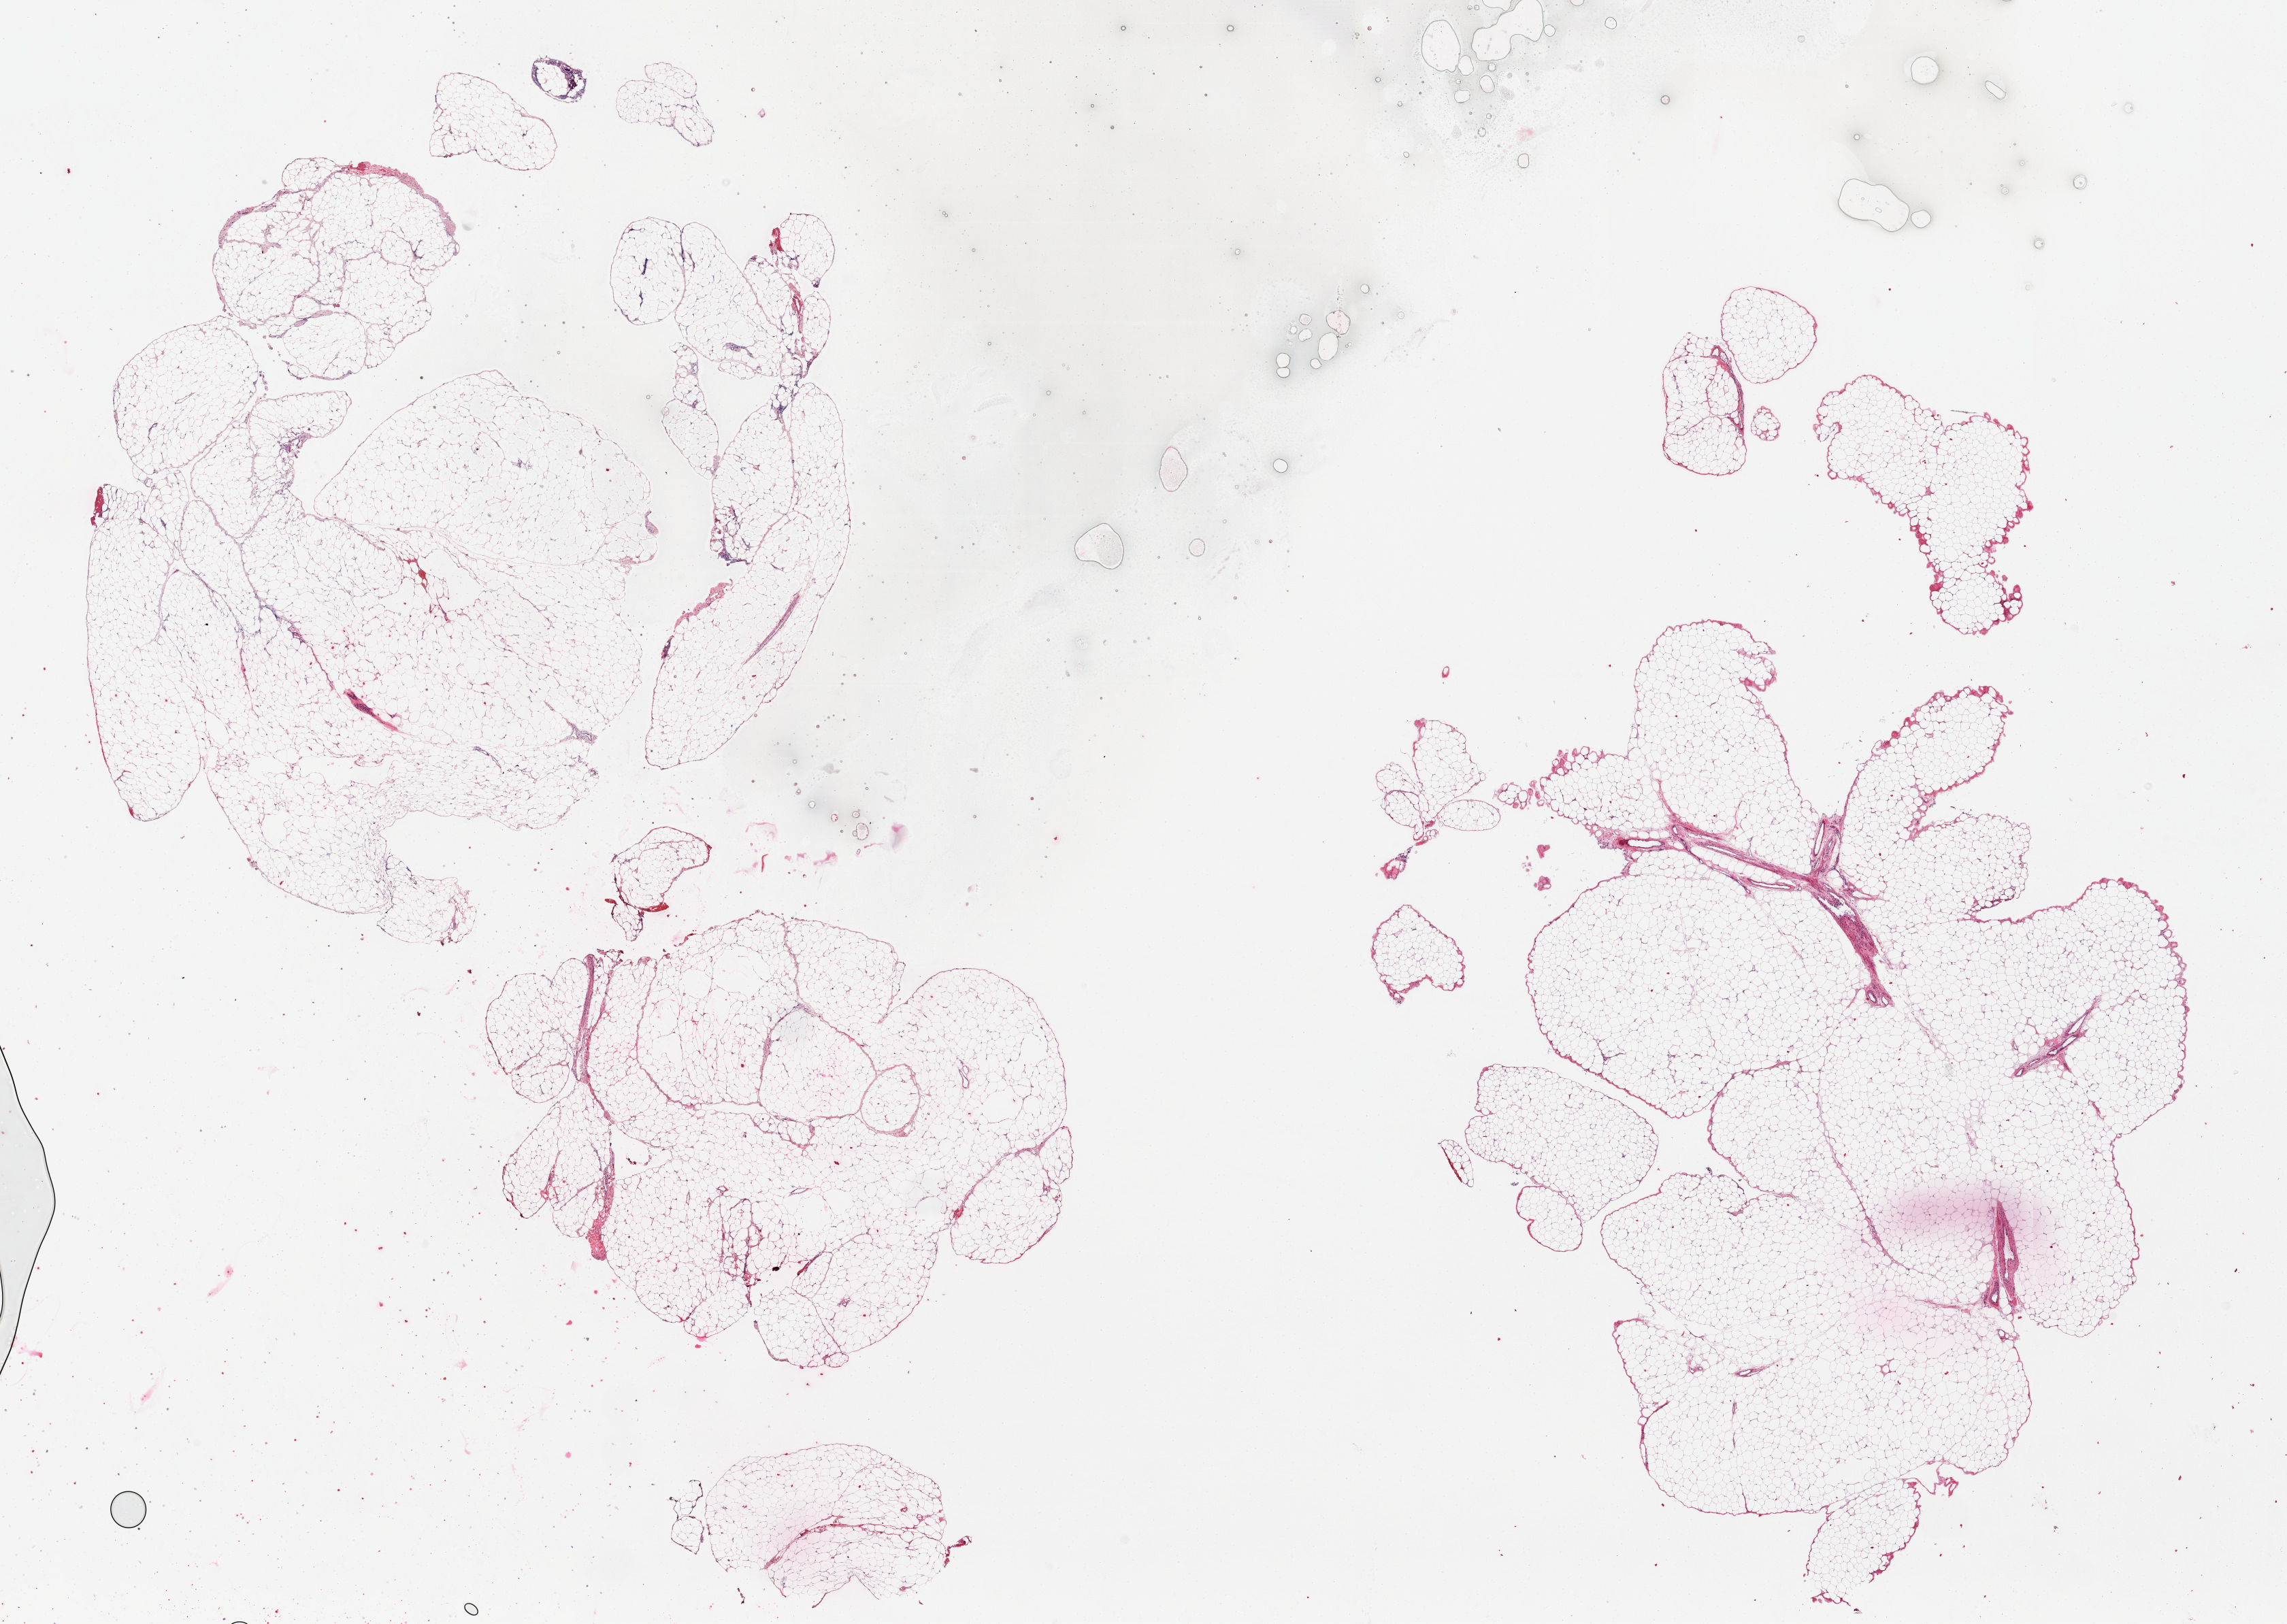
Whole-slide image, hematoxylin and eosin (H&E) stain, low-resolution overview of the scanned area, about 26.6 x 18.9 mm; PAXgene-fixed, paraffin-embedded tissue; target tissue: omentum; tissue donor sample. Donor: male.
• pathologist's review note for this sample: 2 pieces, 18x10 & 15x9mm